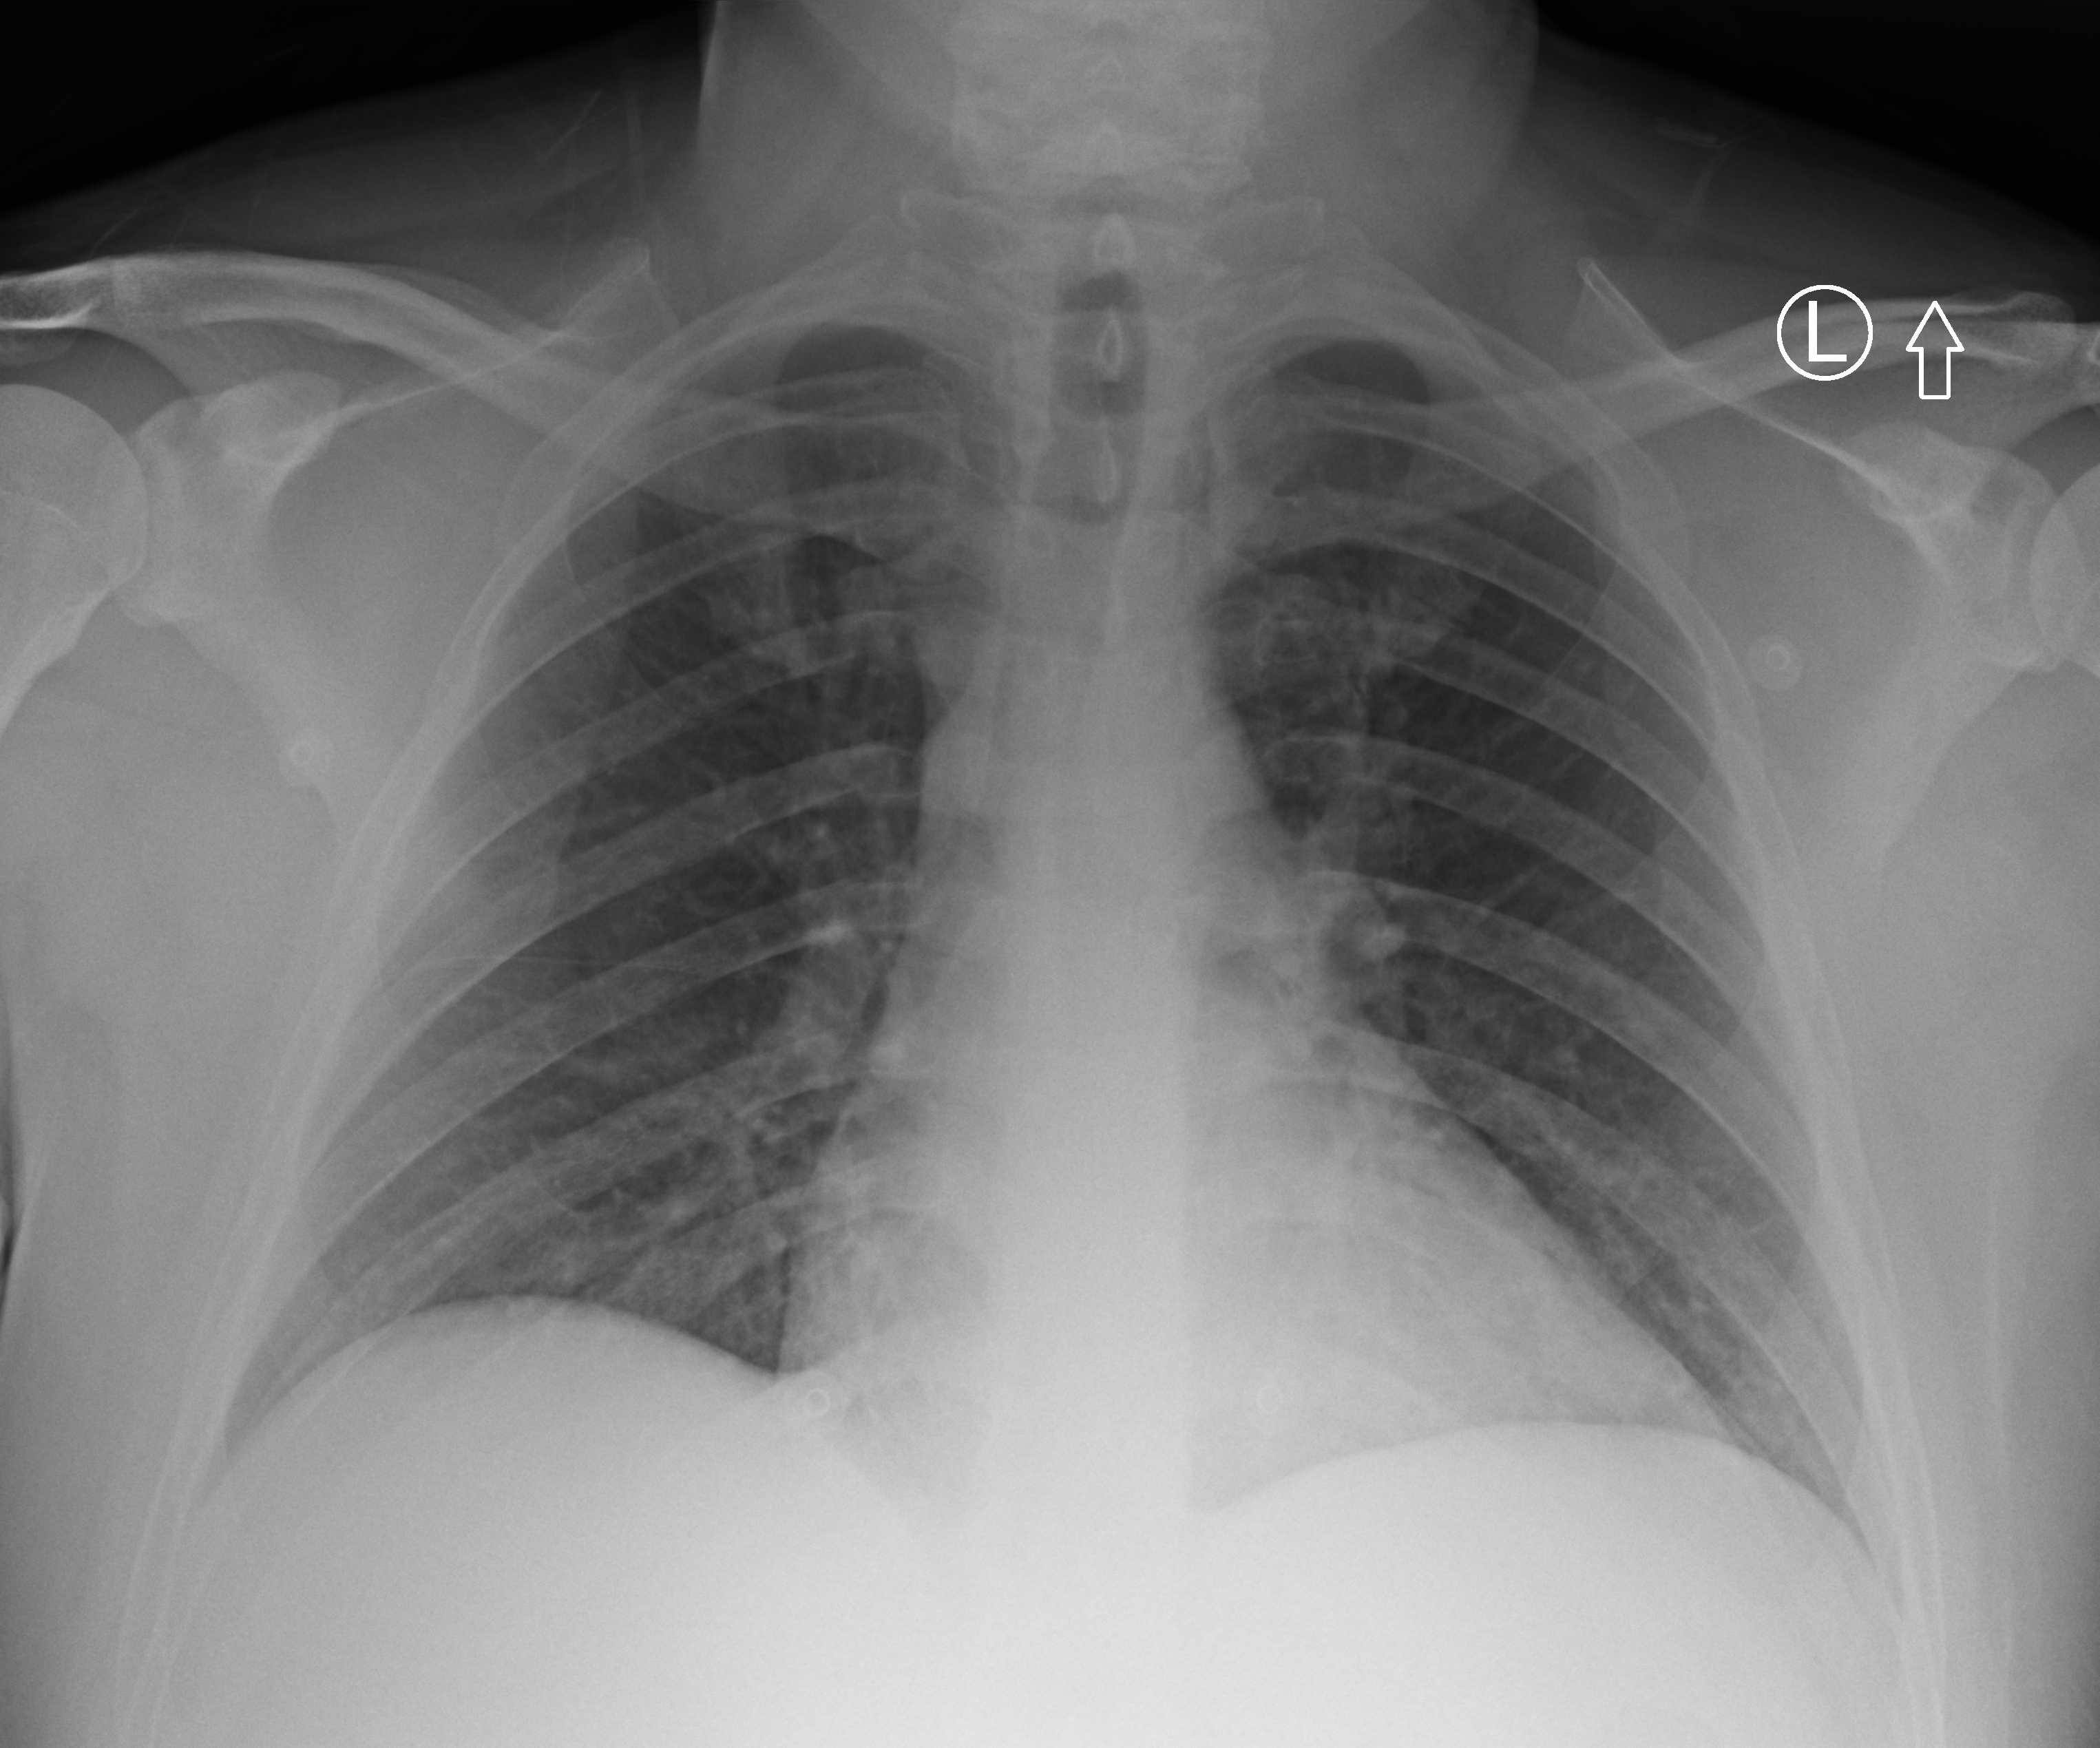
Portable chest radiograph. Male patient hospitalised with COVID-19, age 18–59 years.
Hospital-stay facts (about this admission, not read from this image; timing relative to this image not recorded): mechanically ventilated during this hospital stay: no.